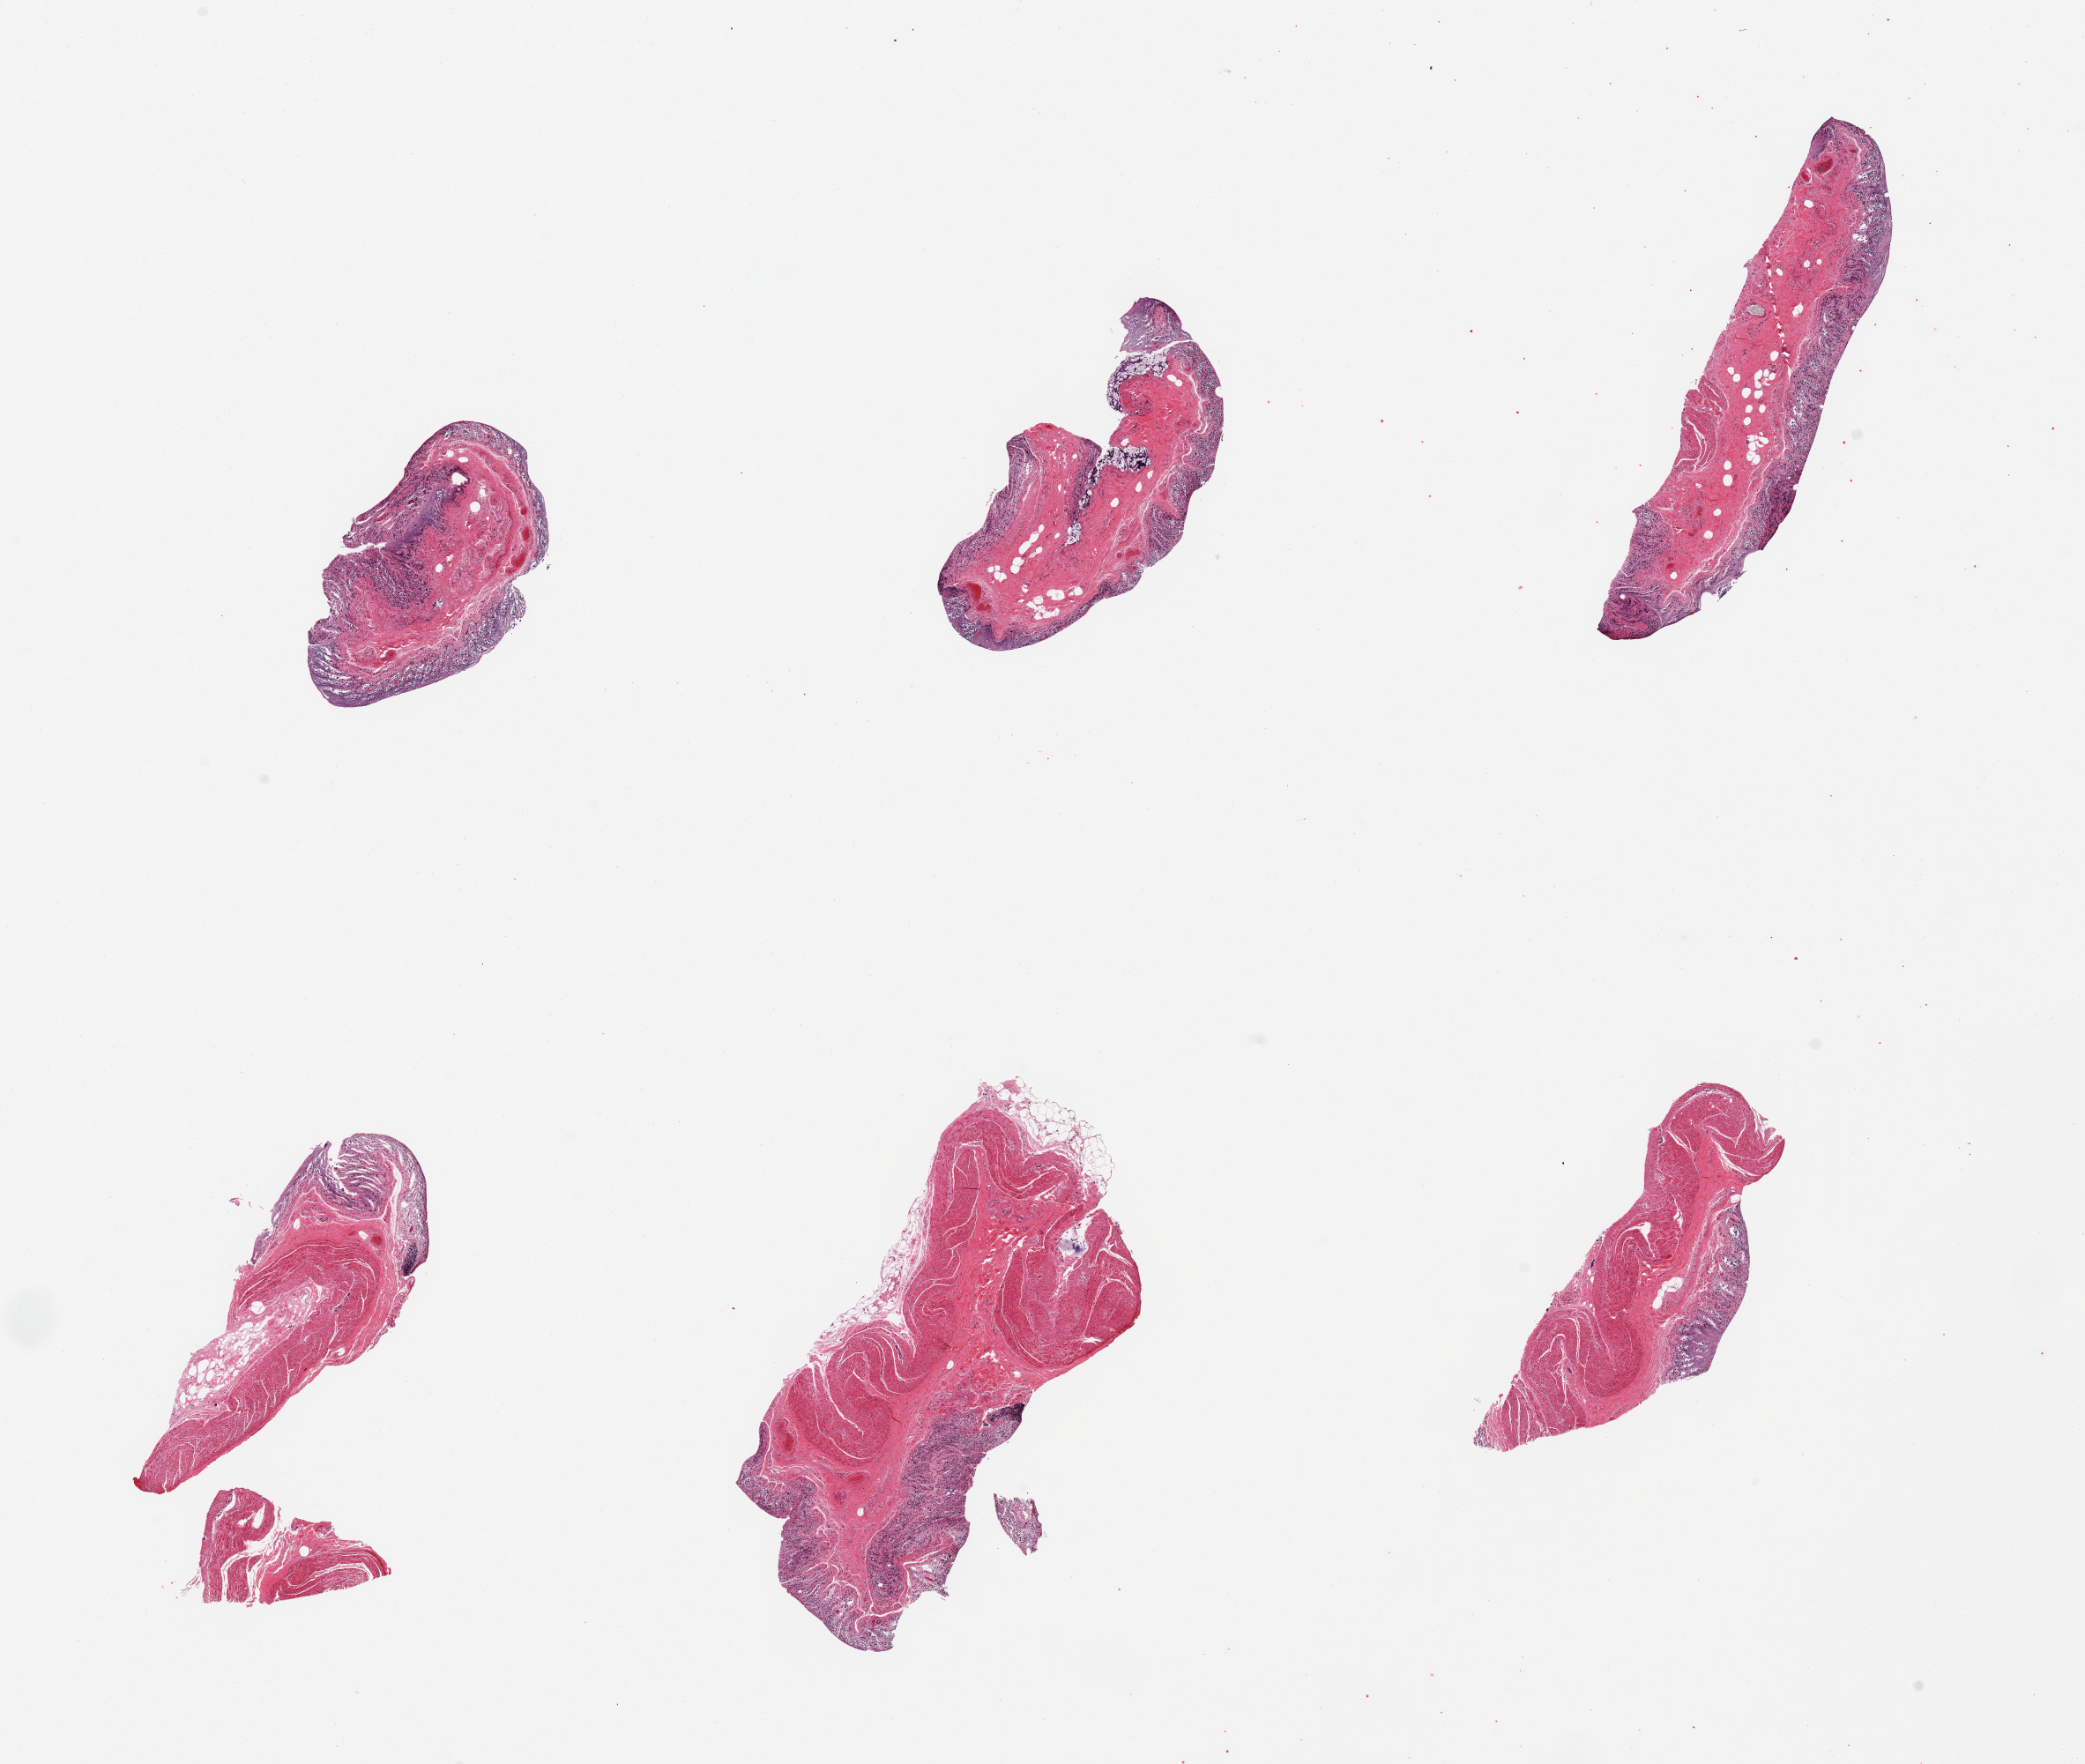
H&E whole-slide image — whole scanned area (about 18.7 x 15.8 mm, from a 20x scan) shown as a low-resolution overview; PAXgene-fixed paraffin-embedded (PFPE) section; sampled site (target tissue): transverse colon; tissue donor sample.
Pathologist's review note for this sample: 6 pieces; autolyzed mucosa and muscularis.